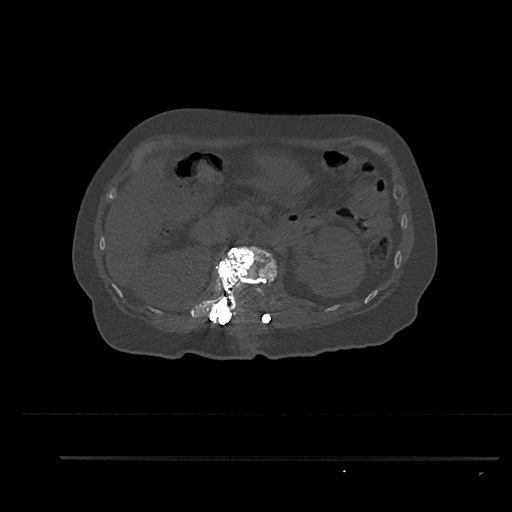
CT including the spine, one axial slice. Position 213 of 797 along the scan axis. 120 kVp. Bone window (W 1800 / L 400 HU). 512 × 512 image matrix, field of view 408 × 408 mm. Female patient, age 44 years. From the clinical record (not read from this slice): primary cancer: renal.
Outlined on this slice (semi-automatically segmented with operator editing):
- L1 vertebra: bounding box <204,246,277,323> (left, top, right, bottom; pixels)